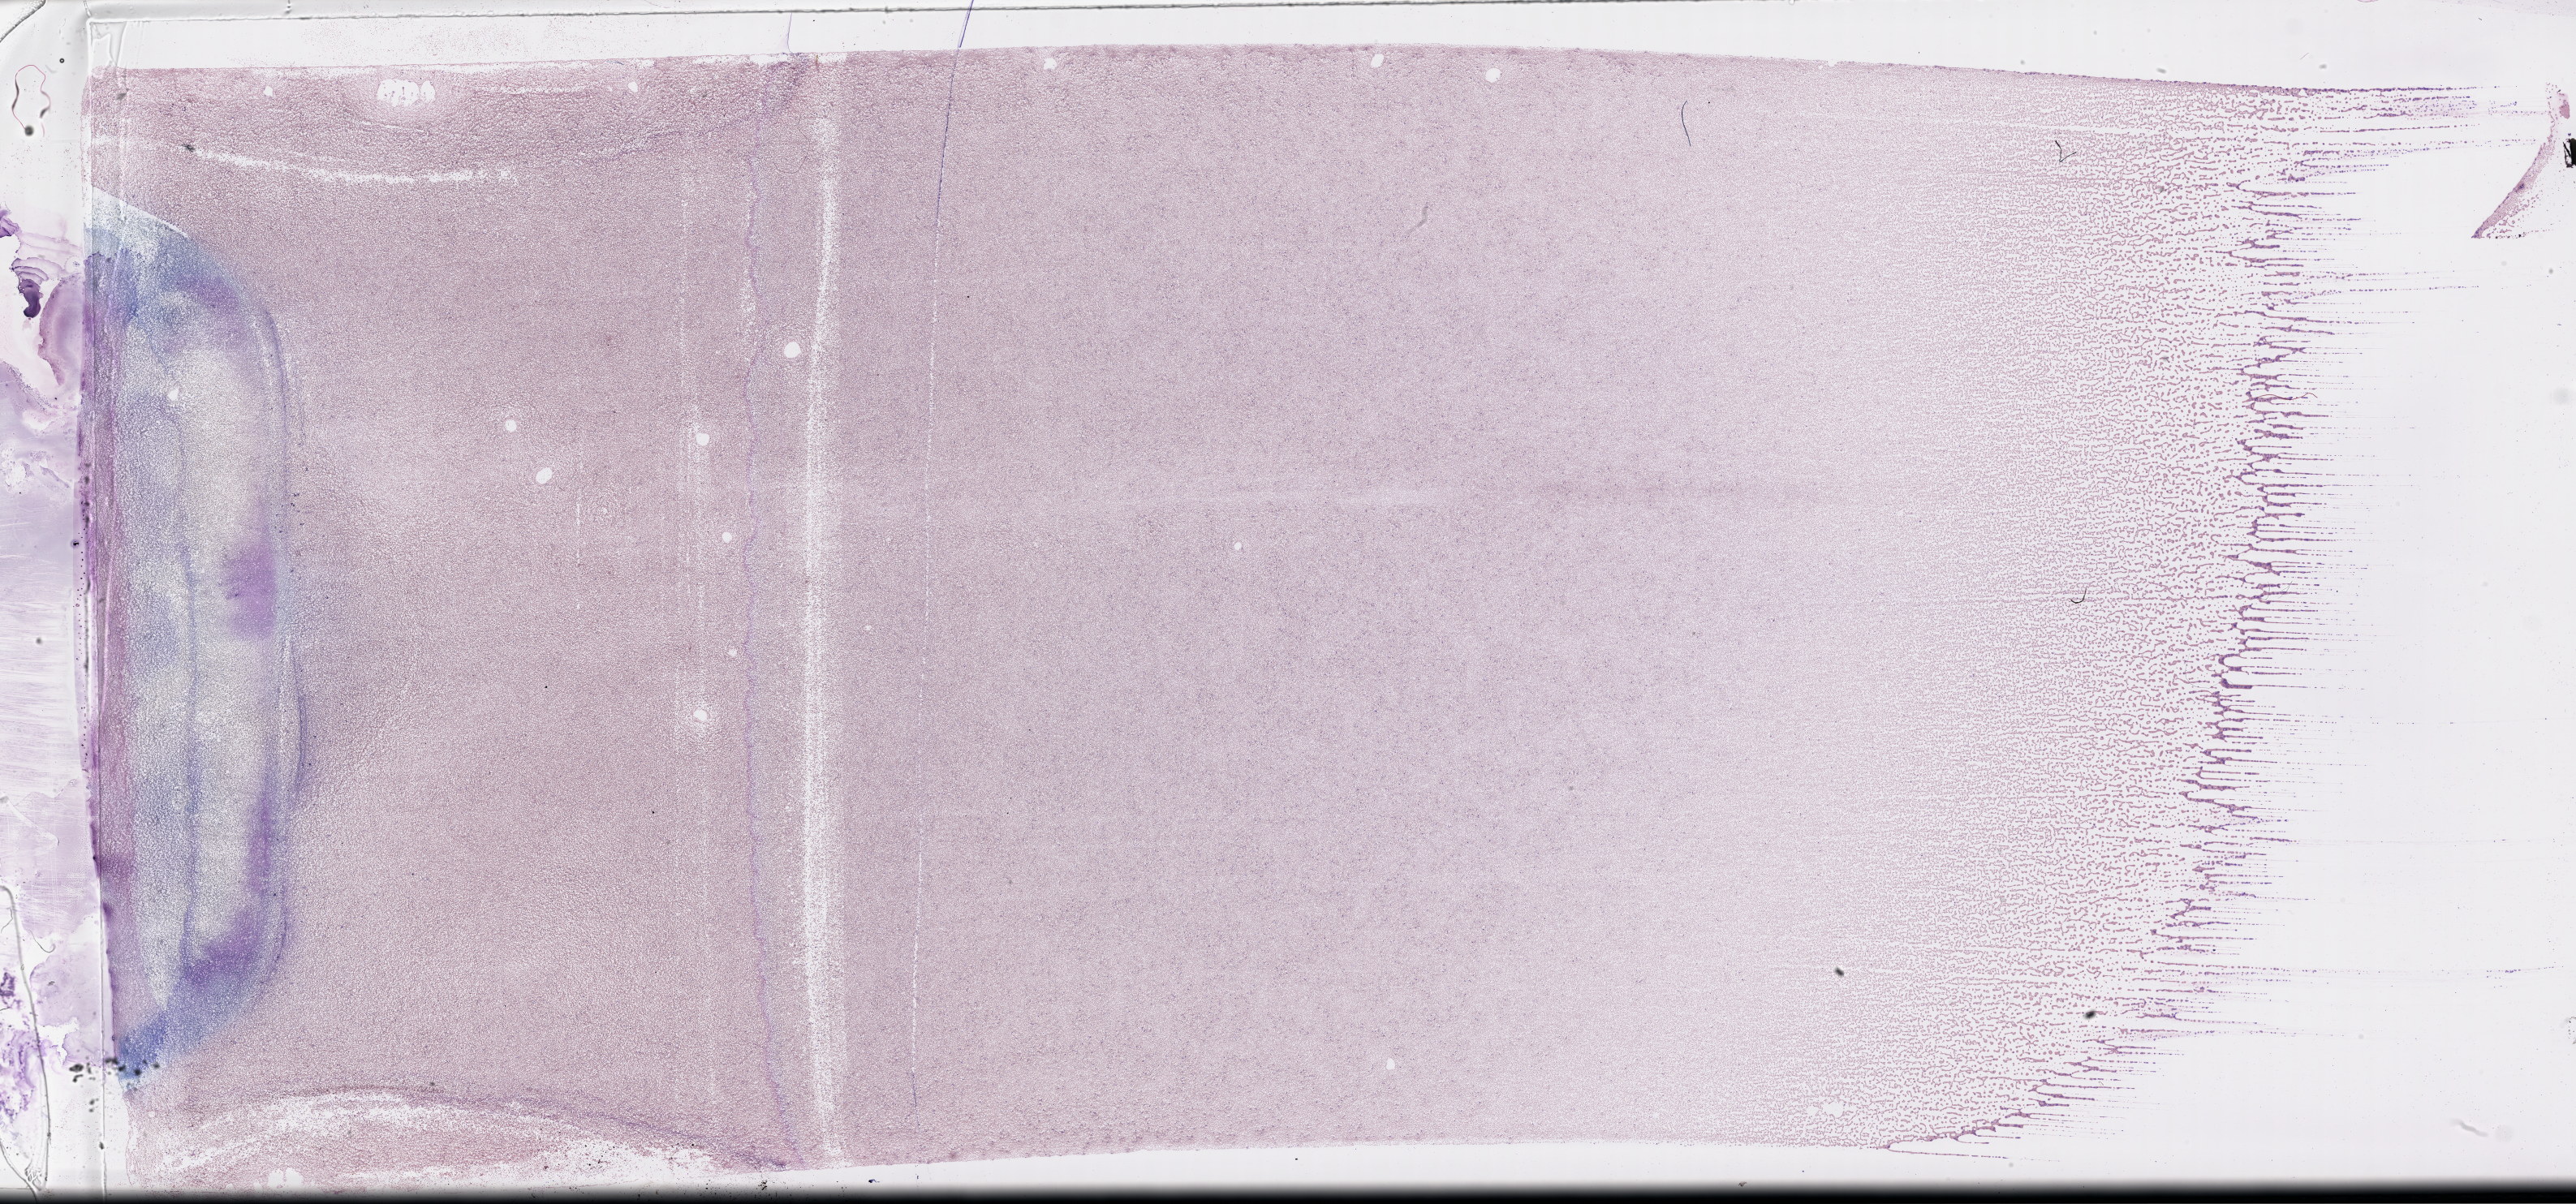
Digitized H&E-stained tissue section (whole slide), shown as a low-resolution overview of the whole scanned area (about 51.3 x 24.0 mm, from a 40x scan). Peripheral blood (leukaemic) sample. Male, 66 y/o.
• FAB classification: M3
• WHO classification: Acute Promyelocytic Leukemia with t(15;17)(q22;q12); PML-RARA
• diagnosis: Acute Myeloid Leukemia